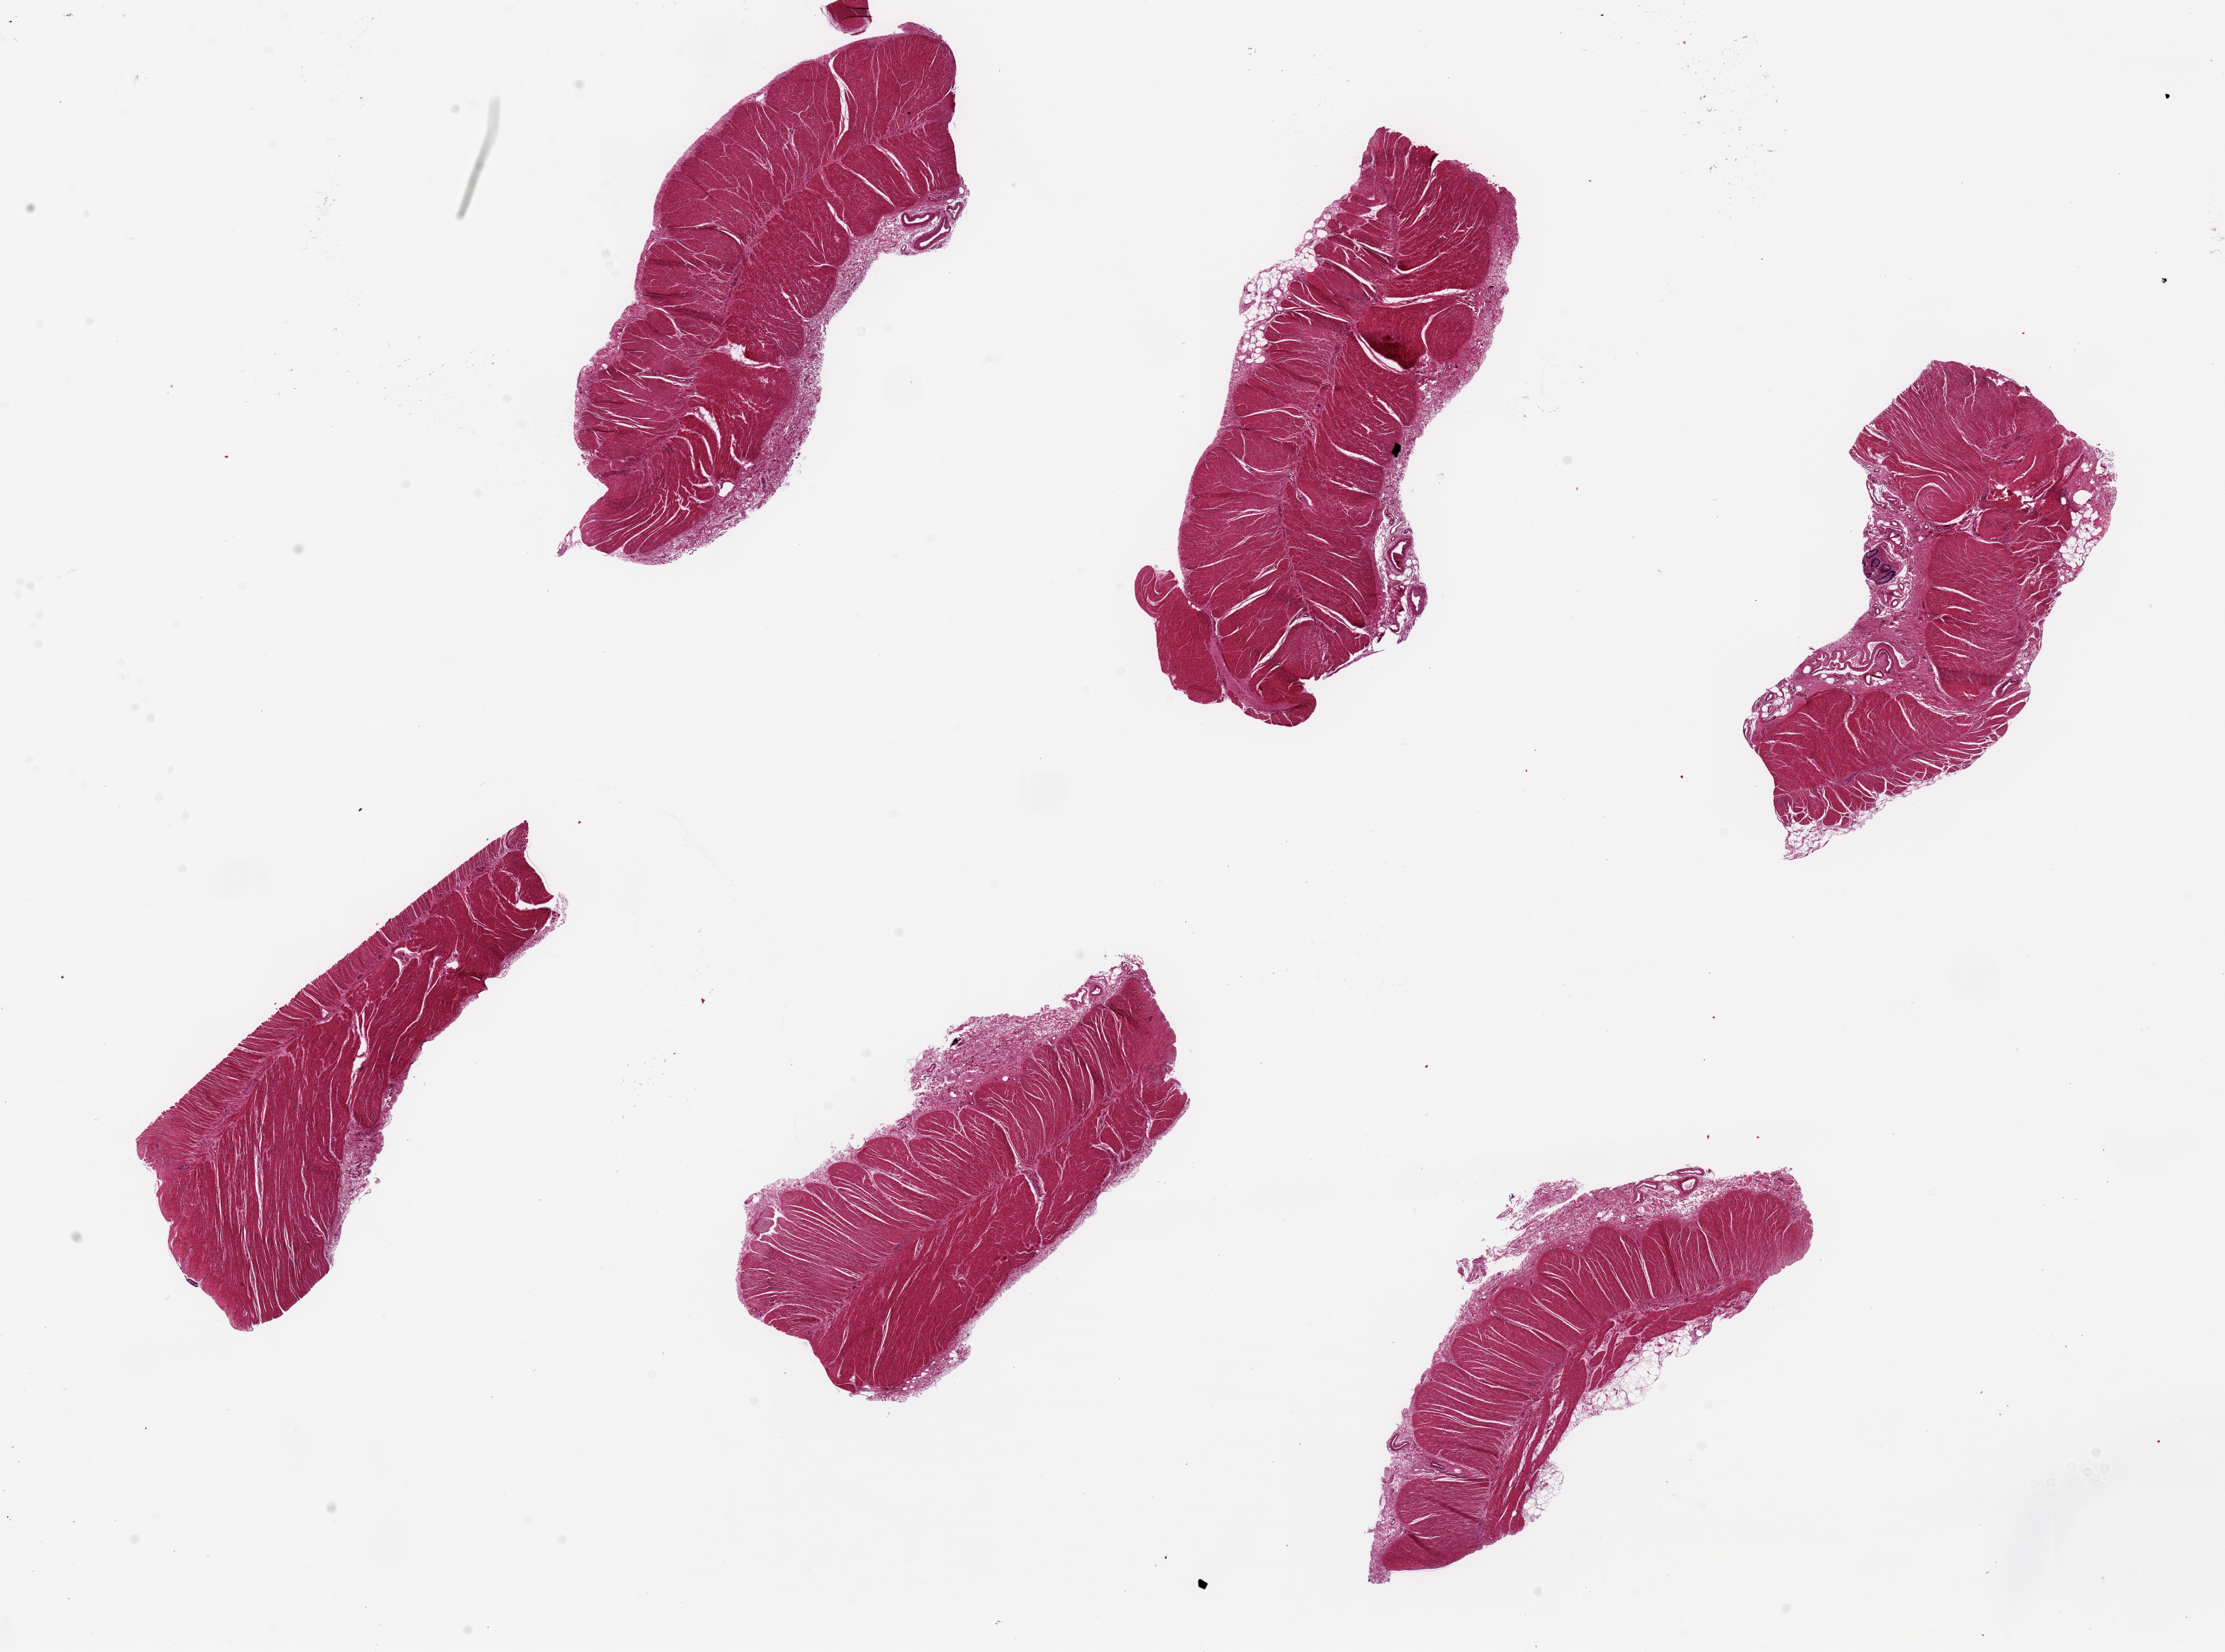
Digitized haematoxylin and eosin-stained section — low-resolution overview of the scanned area, about 25.6 x 19.0 mm (from a 20x scan). PAXgene-fixed, paraffin-embedded tissue. Sampled site (target tissue): sigmoid colon. Donor tissue sample. Donor sex: male.
Review note (as recorded): 6 pieces, up to 7x3mm; well dissected muscularis.